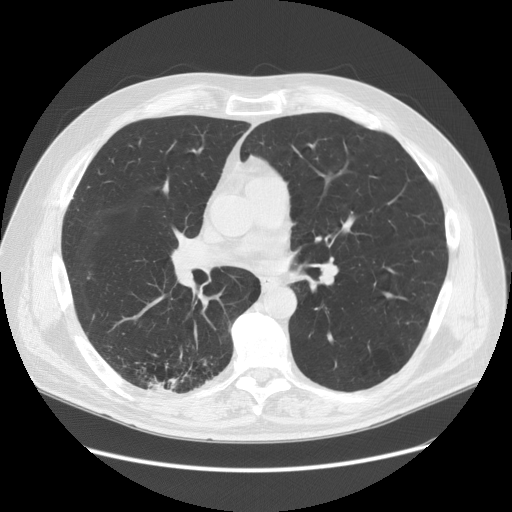
Low-dose screening chest CT, axial slice. First (baseline) screen. Lung window (W 1500 / L -600 HU). 120 kVp. Slice 73 of 149 in the series. 512 × 512 image matrix, field of view 400 × 400 mm. Male participant, aged 68 years at enrolment.
Expert-annotated lung lesion, bounding box [x1, y1, x2, y2] px = [129, 343, 226, 415]. Screening reader's record for this exam (one nodule recorded; not confirmed to be the boxed lesion): non-calcified nodule or mass ≥4 mm, right lower lobe, 37 × 20 mm, spiculated (stellate) margins, soft tissue attenuation. Official screen result: positive, change unspecified: nodule(s) >= 4 mm or enlarging nodule(s), mass(es), or other non-specific abnormalities suspicious for lung cancer. Participant outcome: lung cancer diagnosed 24 days after this screen — adenosquamous carcinoma, right lower lobe, poorly differentiated (G3), stage IIIA (AJCC 6th edition), 30 mm at pathology.